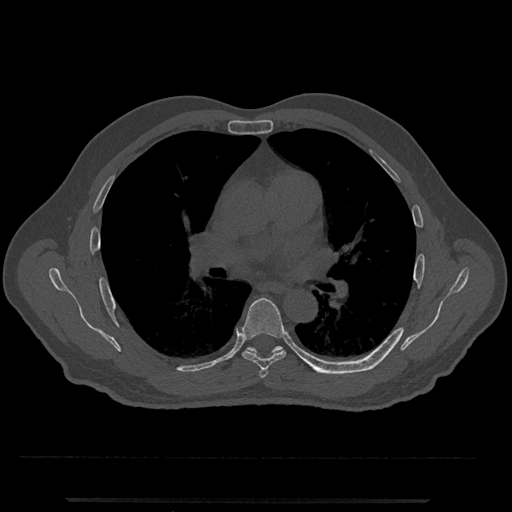
CT including the spine, one axial slice; position 727 of 797 along the scan axis; 120 kVp; bone window (W 1800 / L 400 HU); 512 × 512 image matrix, field of view 419 × 419 mm. Male patient, age 63 years. From the clinical record (not read from this slice): primary cancer: prostate.
Annotated regions visible in this slice (semi-automatic segmentation, software-assisted and operator-edited):
- T5 vertebra: bounding box (x1, y1, x2, y2) in pixels: (259, 369, 268, 378)
- T6 vertebra: (241, 298, 286, 370)
- T7 vertebra: (246, 346, 326, 374)